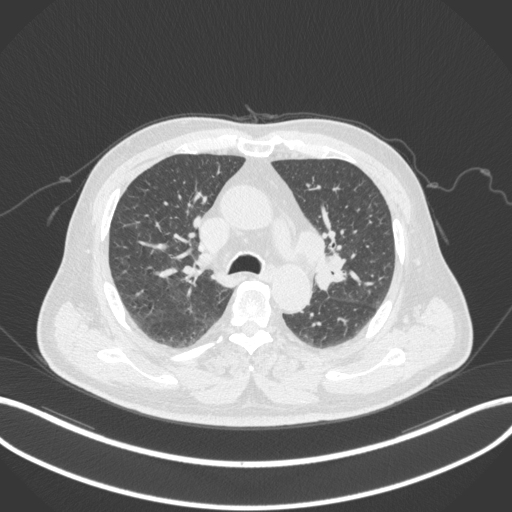
Chest CT, one axial slice; position 195 of 286 along the scan axis; reconstruction kernel B31f; 120 kVp; lung window (W 1500 / L -600 HU); 1 mm slice thickness; 512 × 512 image matrix, field of view 400 × 400 mm. Patient: male, 67 years. From the clinical record (not read from this slice): clinical TNM (as recorded): T2a N1 M0.
Structures marked on this image (bounding box drawn by a radiologist):
- lung tumour (recorded histology: adenocarcinoma): bounding box [x1, y1, x2, y2] px = [311, 251, 351, 293]